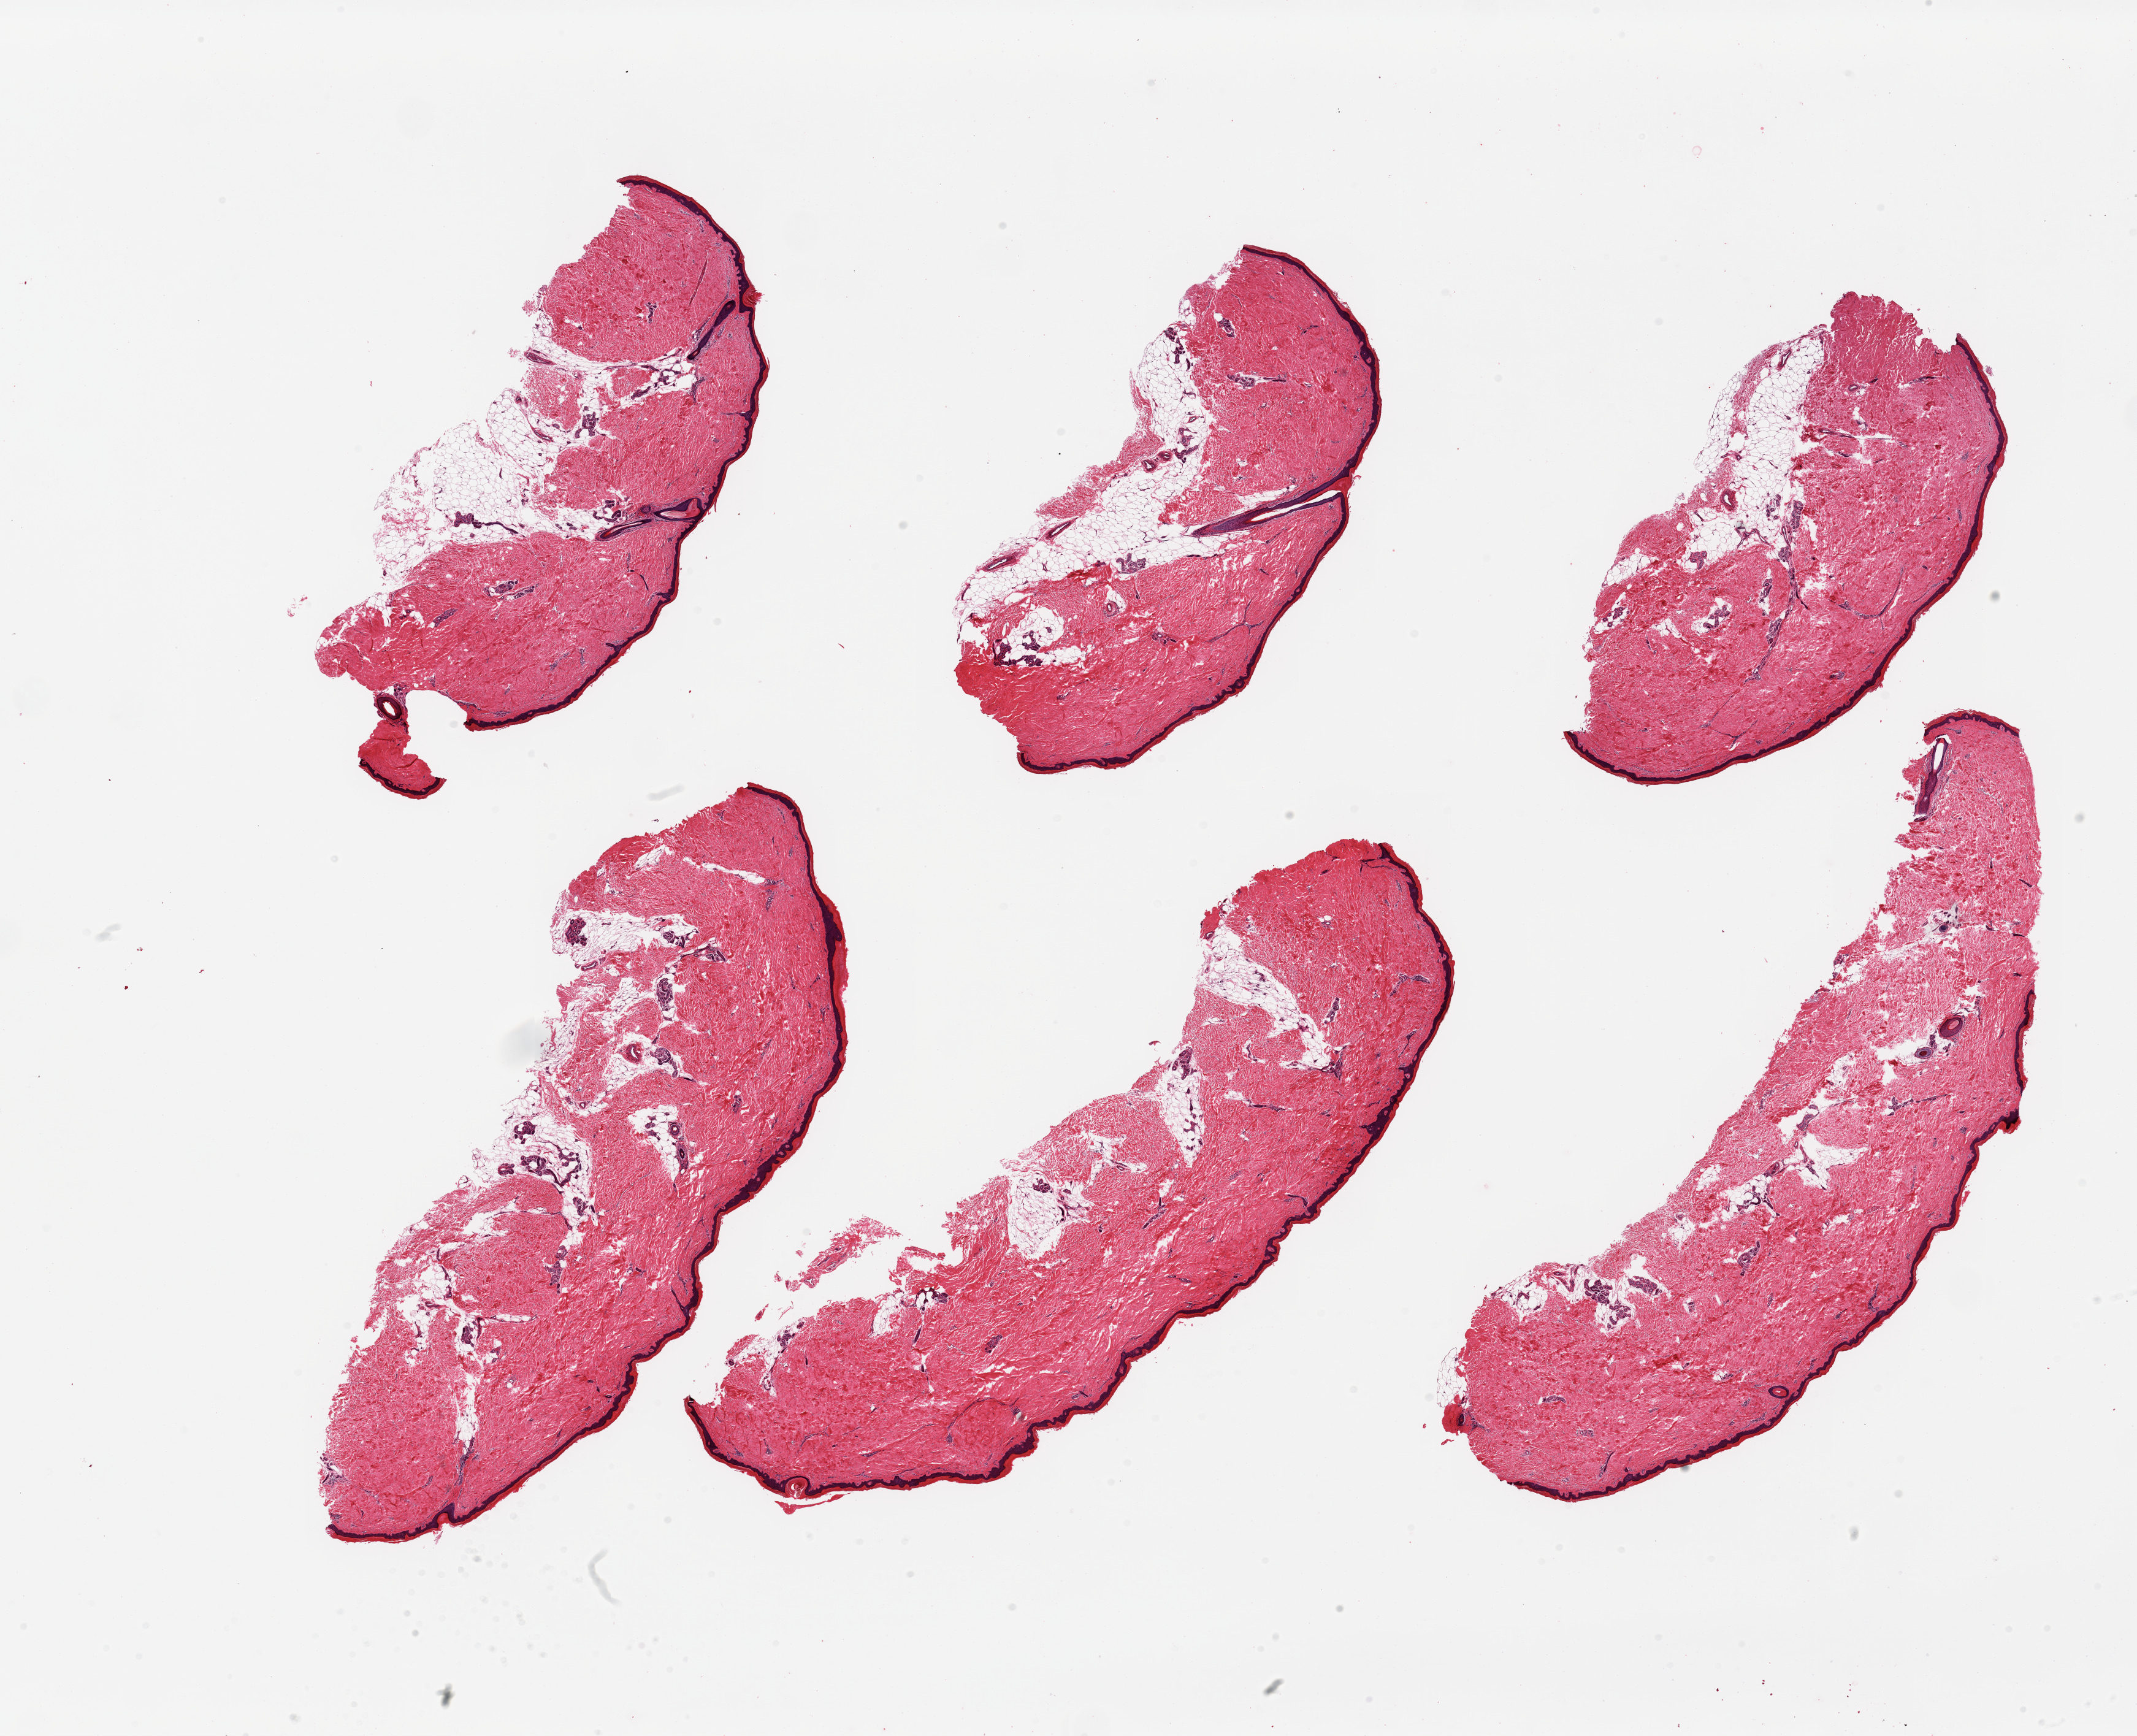
Digitized haematoxylin and eosin-stained section — whole scanned area (about 27.6 x 22.4 mm) shown as a low-resolution overview. PAXgene-fixed, paraffin-embedded tissue. Section of skin of lower leg (target tissue). Donor tissue sample.
Pathologist's review note for this sample: 6 pieces, focal adherent fat up to ~1mm; squamous epithelium is ~60 microns.